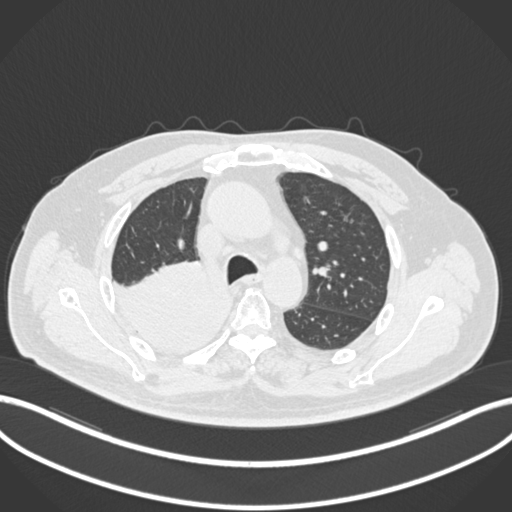
Chest CT, one axial slice; position 141 of 218 along the scan axis; 120 kVp; lung window (W 1500 / L -600 HU); 512 × 512 image matrix, field of view 400 × 400 mm. Male patient, age 68 years. From the clinical record (not read from this slice): clinical TNM (as recorded): T2a N0 M0.
Outlined on this slice (rectangle marked by the reading radiologist):
- lung tumour (recorded histology: adenocarcinoma): bounding box [x1, y1, x2, y2] px = [109, 261, 230, 362]